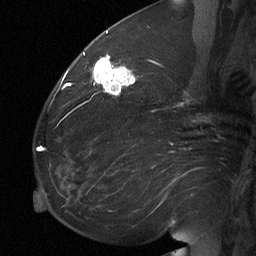
Breast MRI (dynamic contrast-enhanced), one sagittal slice; position 28 of 64 along the scan axis; dynamic contrast-enhanced study with each time point stored as its own series, time point 2 of 3 at this slice position (early post-contrast, ordered by acquisition time); 1.5 T; TE 4.8 ms, TR 27 ms; 2 mm slice thickness; 256 × 256 image matrix, field of view 200 × 200 mm. Patient: female, 60 years. Case-level facts recorded for this patient, not image findings: setting: breast cancer imaged before/during neoadjuvant chemotherapy; receptor status: HR-positive, HER2-negative.
Annotated regions visible in this slice (semi-automatic segmentation, software-assisted and operator-edited):
- analysis volume of interest (the breast-tissue region the enhancement analysis was run in; not a lesion): bounding box (x1, y1, x2, y2) in pixels: (91, 56, 135, 96)
- tumour enhancement mask (voxels above the 90 % enhancement threshold inside the analysis volume of interest): (93, 56, 134, 95)